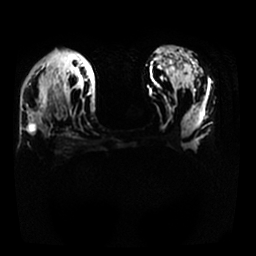
Breast MRI, one axial slice. Diffusion-weighted series; image 2 of 4 stored at this slice position (different b-values; order by instance number). 1.5 T. 4 mm slice thickness. 256 × 256 image matrix, field of view 340 × 340 mm. Female patient.
Structures marked on this image (outlined manually by an expert reader):
- tumour on diffusion-weighted imaging: bounding box [x1, y1, x2, y2] px = [27, 99, 43, 134]